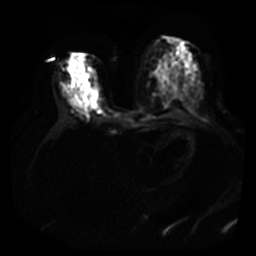
Breast MRI, one axial slice. Slice 20 of 40 in the series (ordered by position). Diffusion-weighted series; image 2 of 4 stored at this slice position (different b-values; order by instance number). 3 T. 5 mm slice thickness. 256 × 256 image matrix. Female patient.
Annotated regions visible in this slice (outlined manually by an expert reader):
- tumour on diffusion-weighted imaging: bounding box <83,92,86,96> (left, top, right, bottom; pixels)